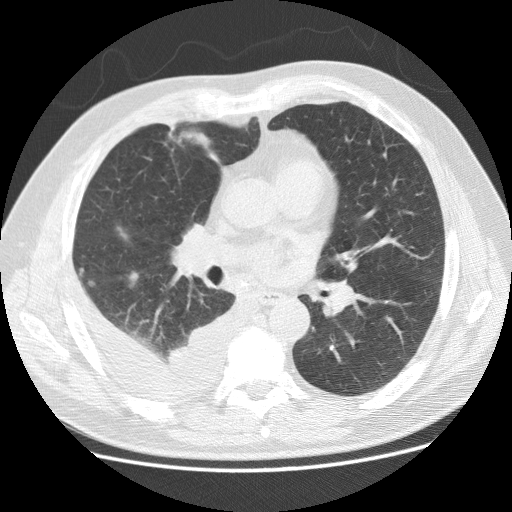
Low-dose screening chest CT, one axial slice; slice 68 of 142 in the series (ordered by position); 120 kVp; lung window (W 1500 / L -600 HU); 2.5 mm slice thickness; 512 × 512 image matrix, field of view 380 × 380 mm.
Annotated regions visible in this slice (manually delineated by an expert):
- lesion 1 (tumor, middle lobe of right lung): box from (x=168, y=129) to (x=210, y=149) px